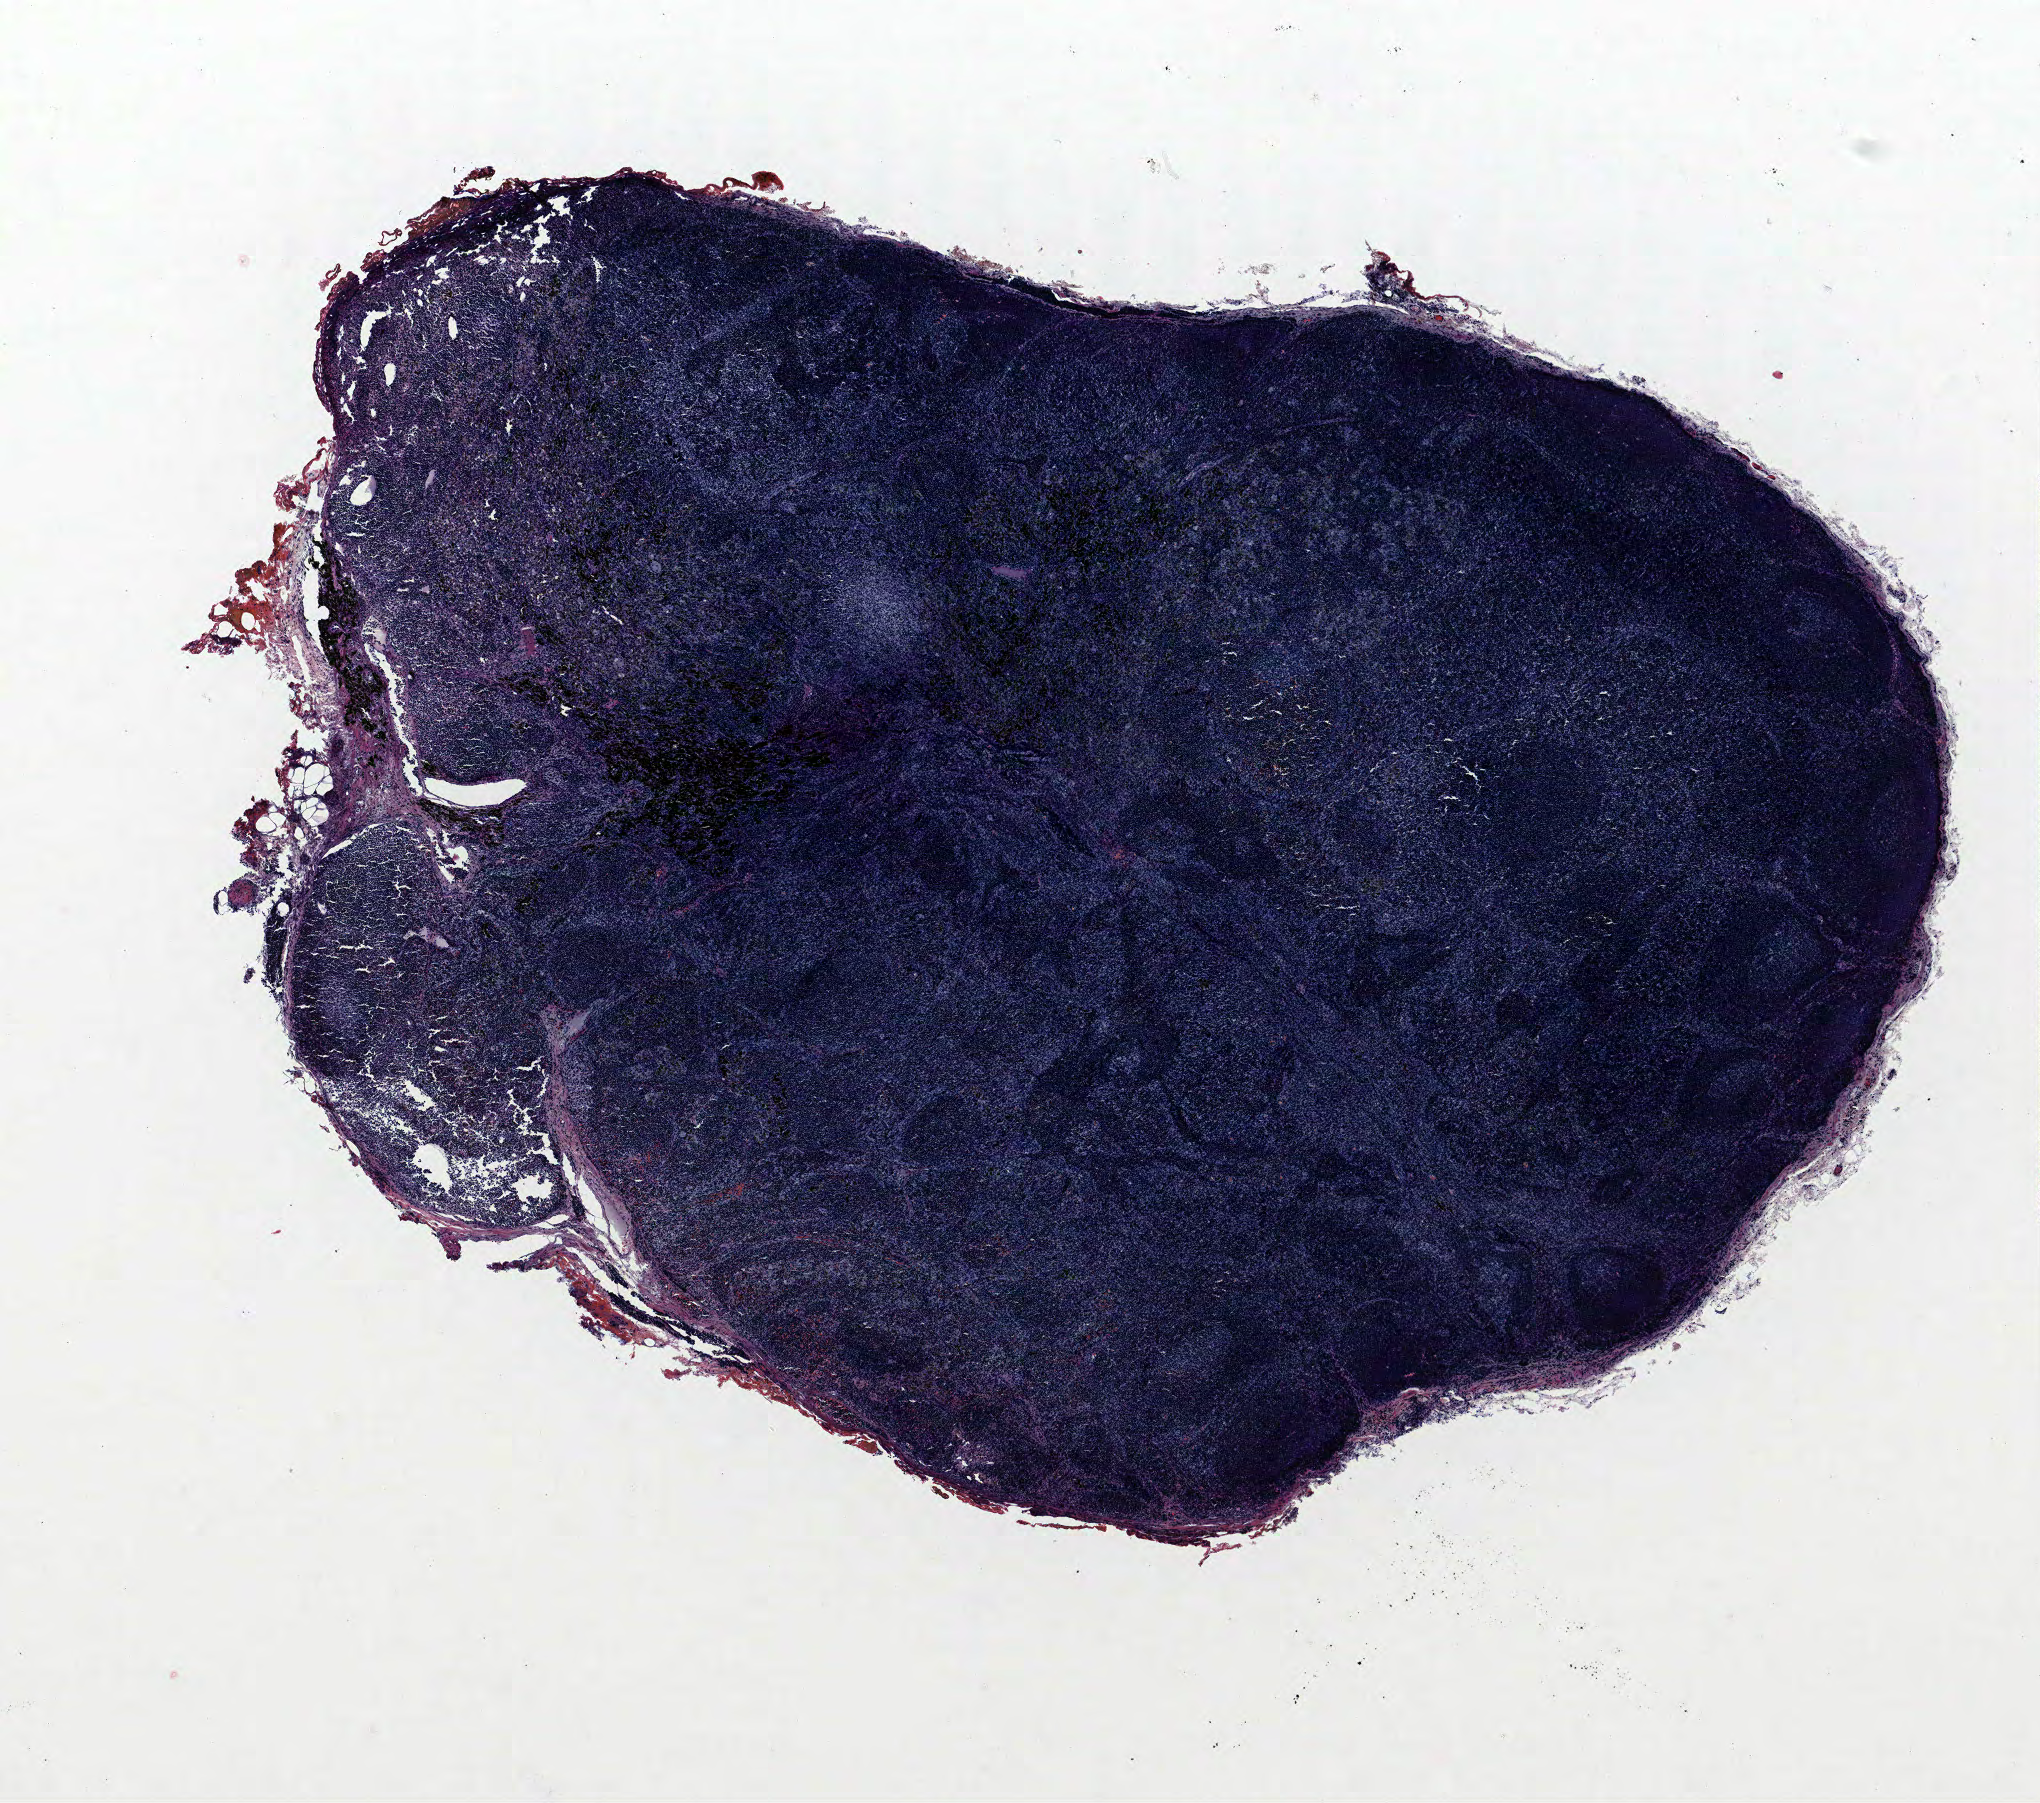
Hematoxylin and eosin (H&E) stained whole-slide image — whole scanned area (about 8.2 x 7.2 mm) shown as a low-resolution overview; formalin-fixed paraffin-embedded (FFPE) section; lung tissue. Male patient, aged 72 at enrolment. Current smoker at enrolment. Grade: moderately differentiated (G2).
Stage (AJCC 6th edition): IIA. Participant's lung-cancer diagnosis: Squamous cell carcinoma, NOS. Tumour size (pathology): 25 mm. Primary tumour location (clinical record): right upper lobe.